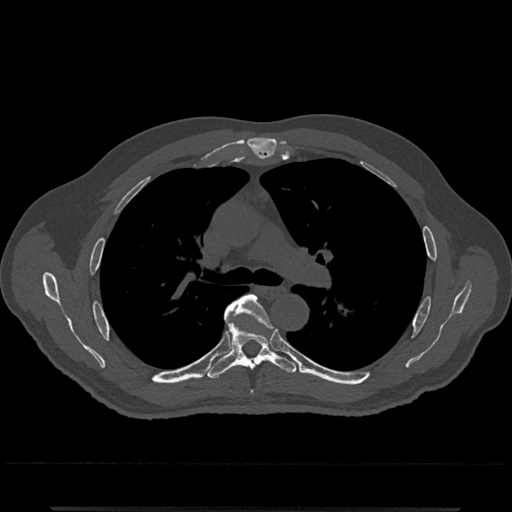
CT including the spine, one axial slice; slice 791 of 797 in the series (ordered by position); reconstruction kernel Br40s/3; bone window (W 1800 / L 400 HU); 0.5 mm slice thickness; 512 × 512 image matrix. Patient: male, 67 years. Case-level facts recorded for this patient, not image findings: primary cancer: prostate.
Structures marked on this image (semi-automatic segmentation, software-assisted and operator-edited):
- T5 vertebra: box from (x=227, y=294) to (x=269, y=320) px
- T6 vertebra: (x=205, y=302)–(x=297, y=379)